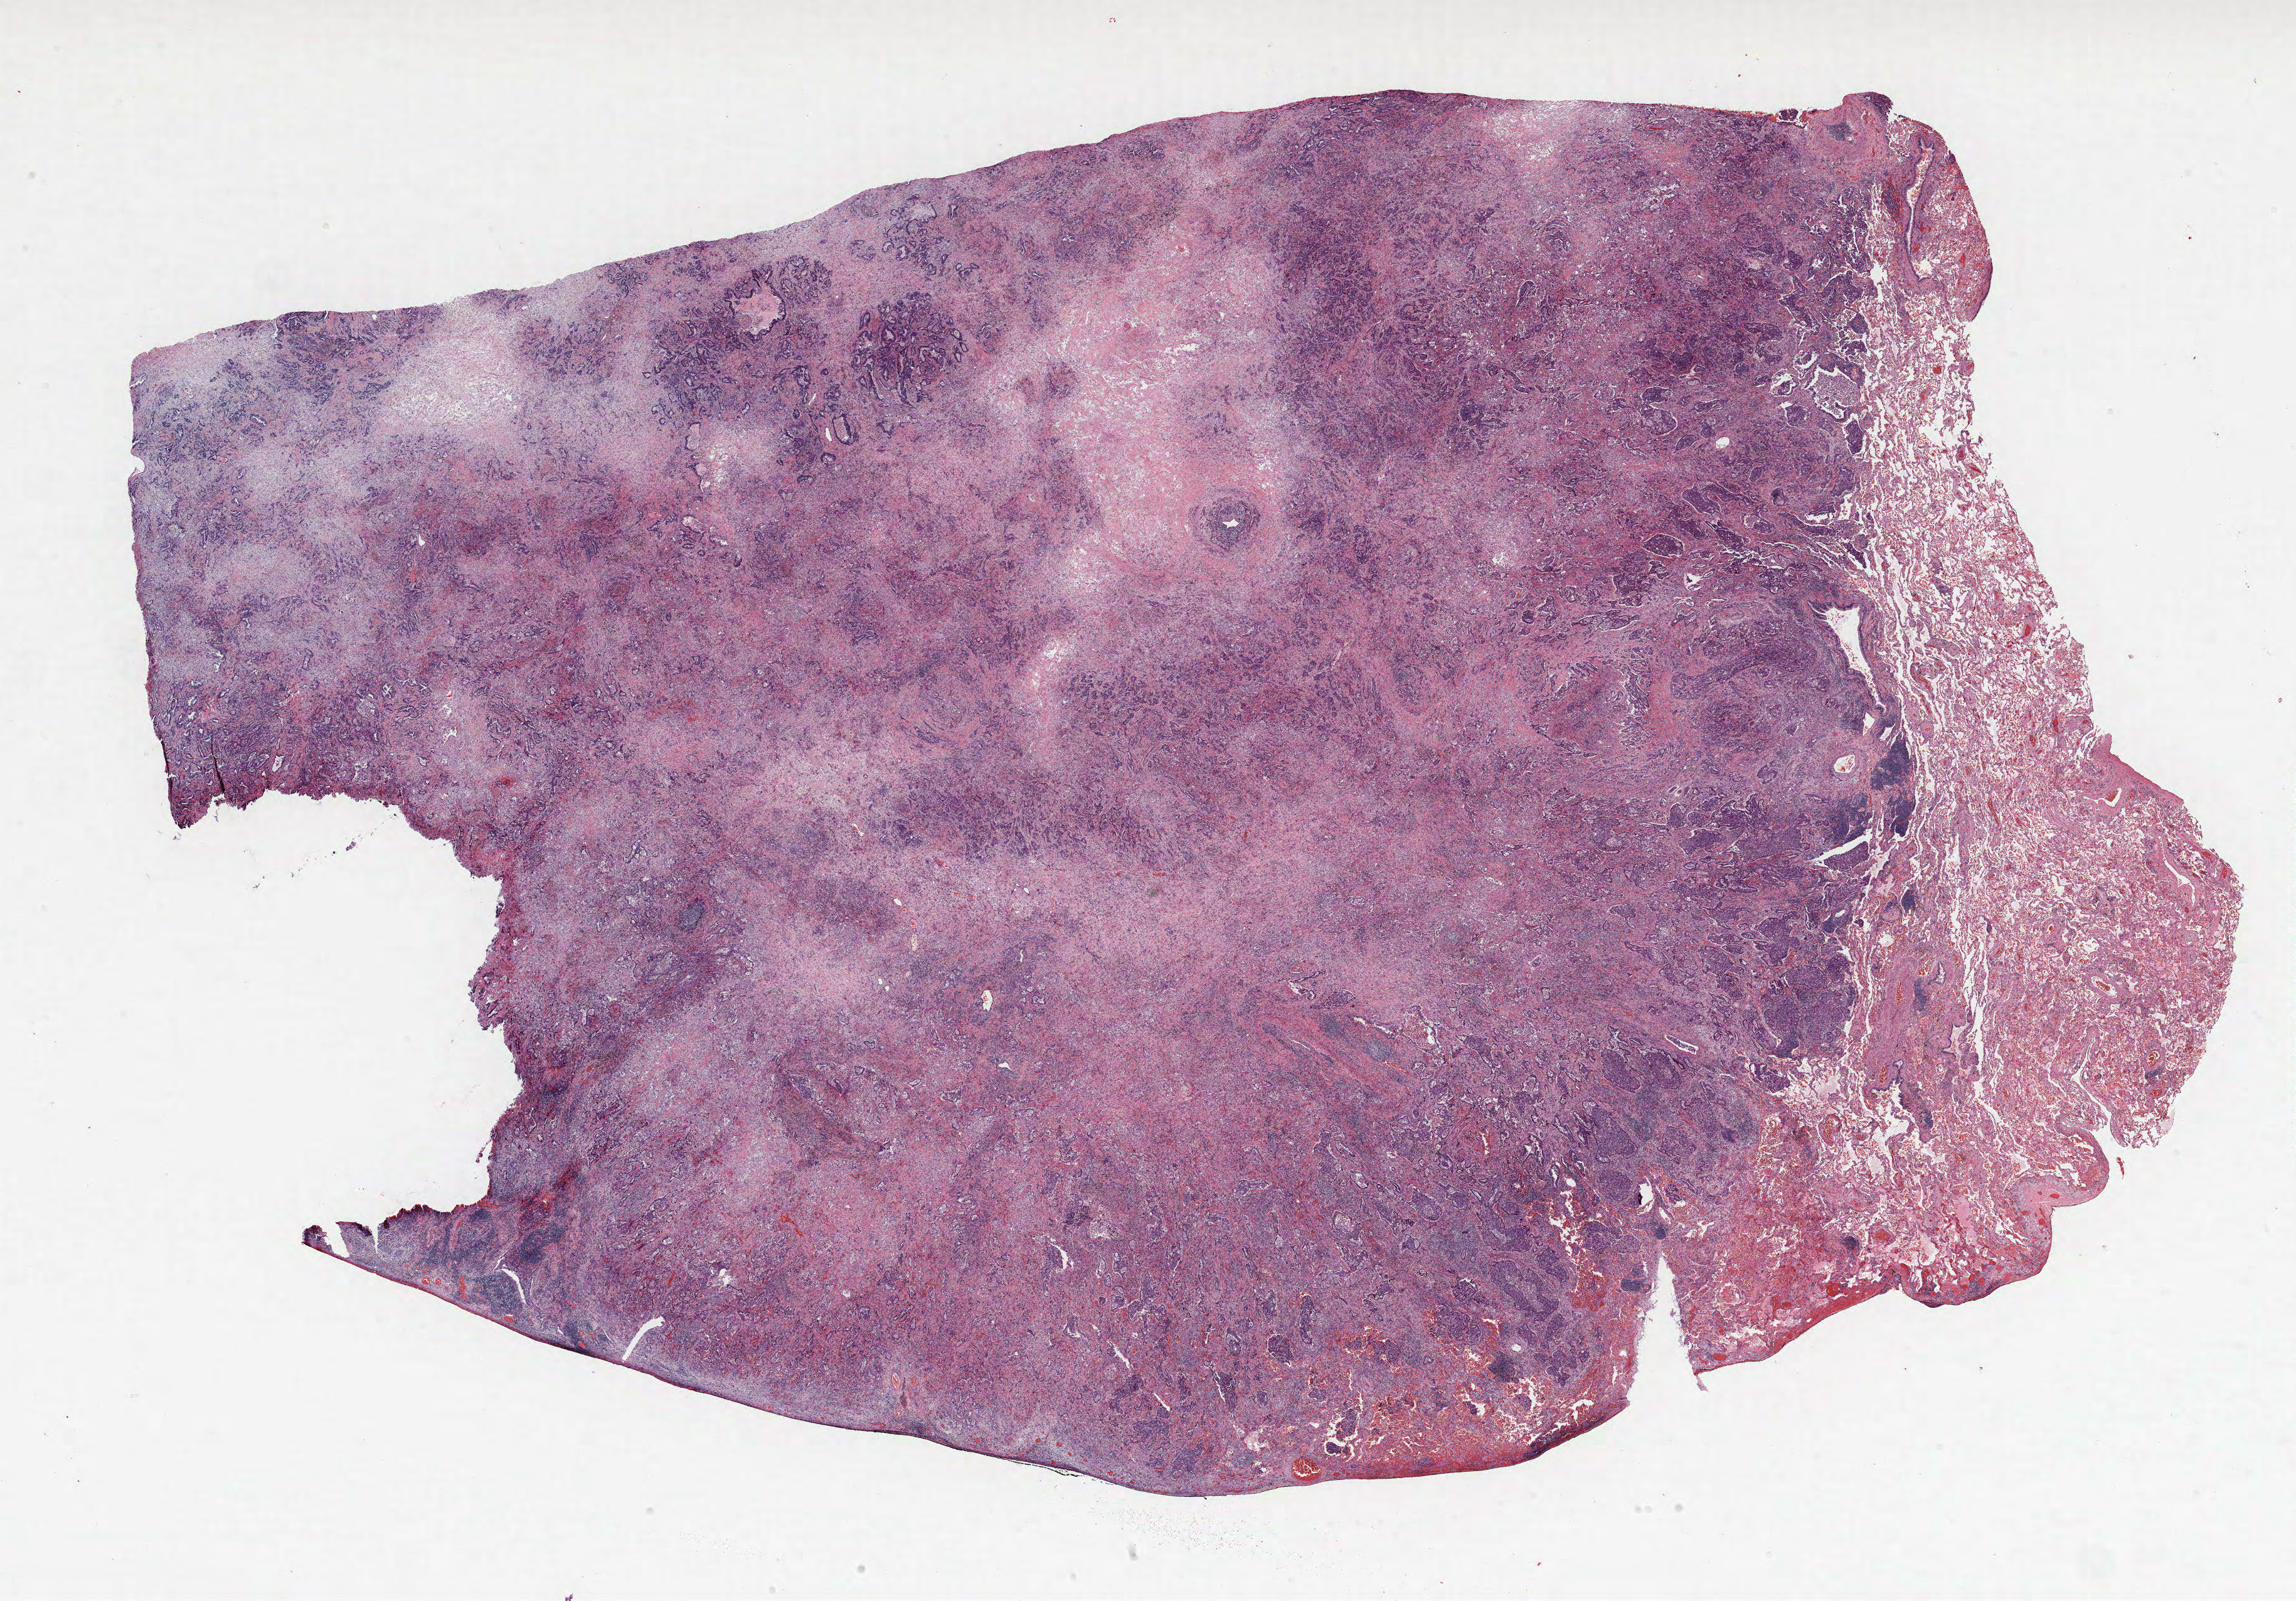
H&E-stained whole-slide image, whole scanned area (about 29.3 x 20.4 mm) shown as a low-resolution overview. FFPE section. Lung. Male patient, aged 66 at enrolment. Former smoker at enrolment.
Participant's lung-cancer diagnosis: Adenocarcinoma, NOS (ICD-O-3 8140/3).